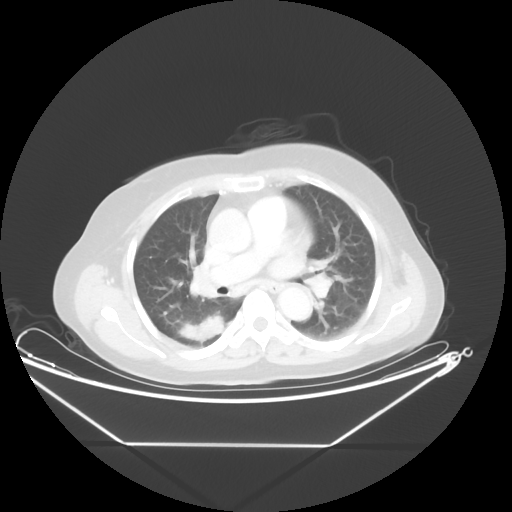
Chest CT, one axial slice; position 27 of 48 along the scan axis; 100 kVp; lung window (W 1500 / L -600 HU); 5 mm slice thickness; 512 × 512 image matrix, field of view 462 × 462 mm. Patient: female, 62 years. From the clinical record (not read from this slice): clinical TNM (as recorded): T1c N0 M0.
Outlined on this slice (rectangle marked by the reading radiologist):
- lung tumour (recorded histology: adenocarcinoma): box from (x=174, y=312) to (x=225, y=350) px